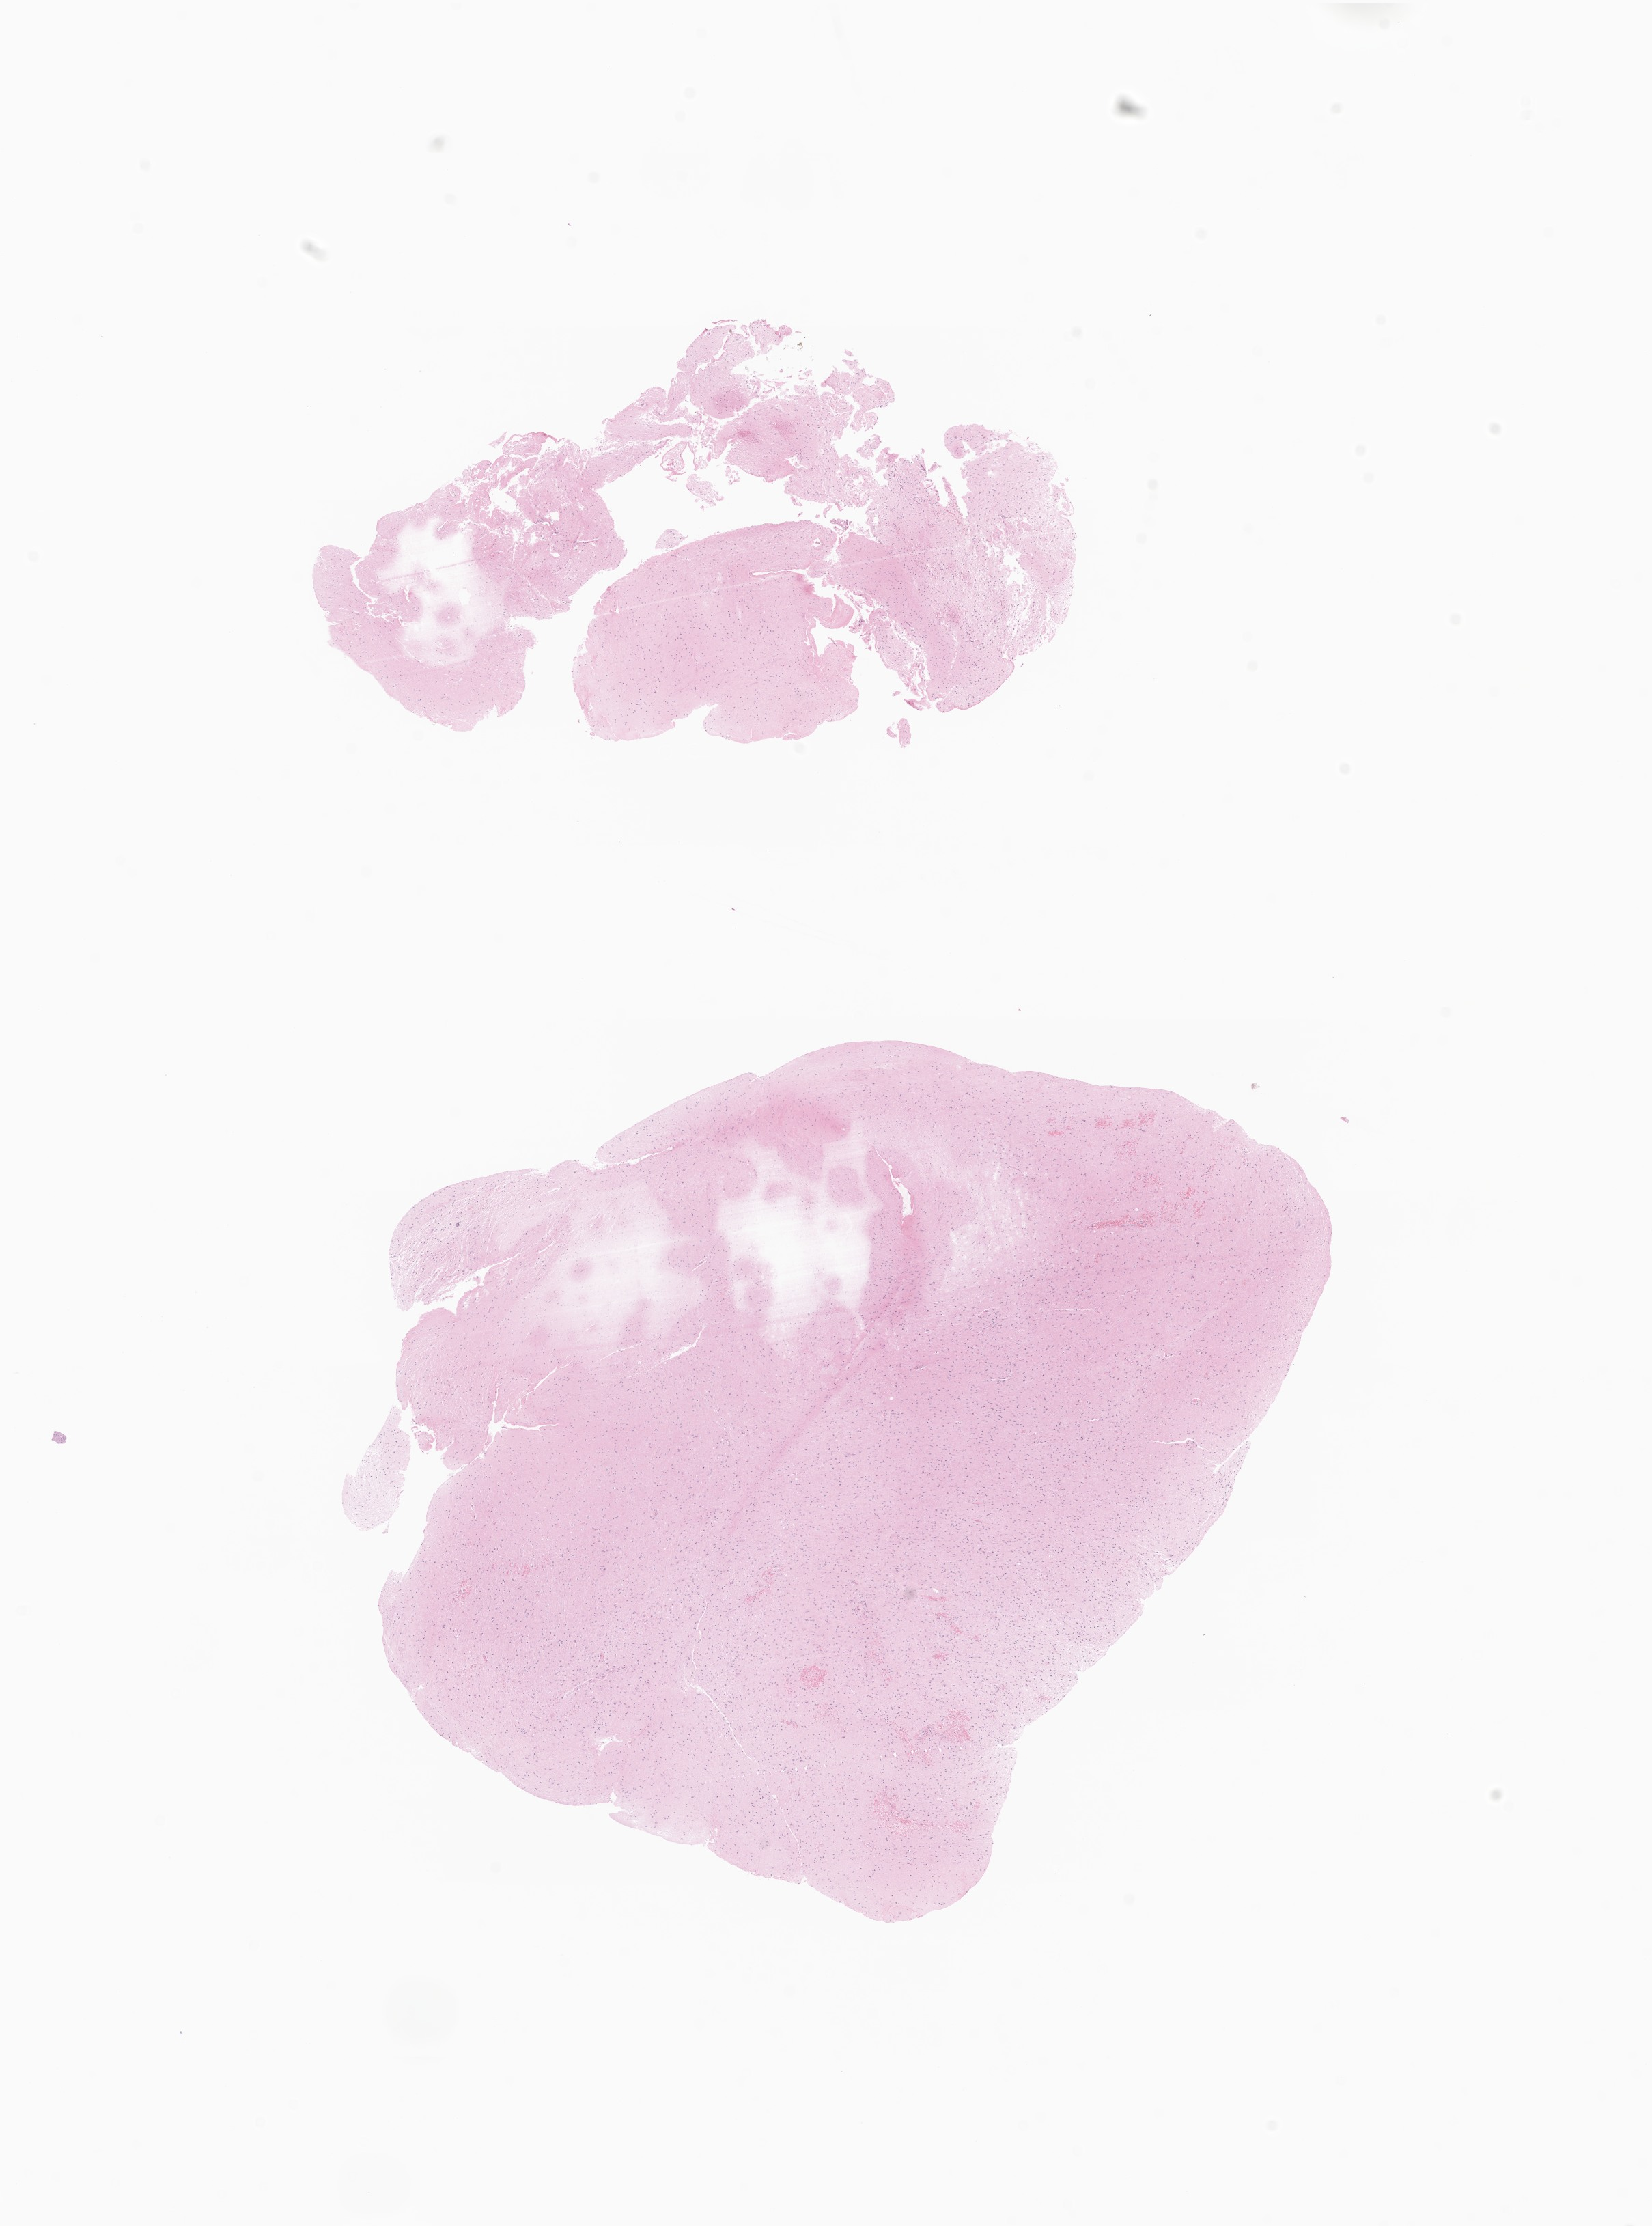
Whole-slide image, H&E stain of tumor tissue from the spinal cord, a low-resolution overview of the entire scanned area, about 10.2 x 13.7 mm. Formalin-fixed paraffin-embedded section. Male patient, age 46 months (3 years 10 months).
Diagnosis: Glioma, malignant.